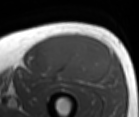
MRI of an extremity soft-tissue mass, one axial slice; position 48 of 86 along the scan axis; MR volume resampled by the dataset authors to the PET/CT grid (not the native acquisition matrix); 139 × 117 image matrix, field of view 136 × 114 mm. Male patient. From the clinical record (not read from this slice): histological type: extraskeletal osteosarcoma; grade: high; site of the primary tumour: thigh.
Annotated regions visible in this slice (expert contour drawn on MRI and transferred to this co-registered scan by the dataset authors):
- gross tumour volume (mass): bounding box <45,34,110,81> (left, top, right, bottom; pixels)